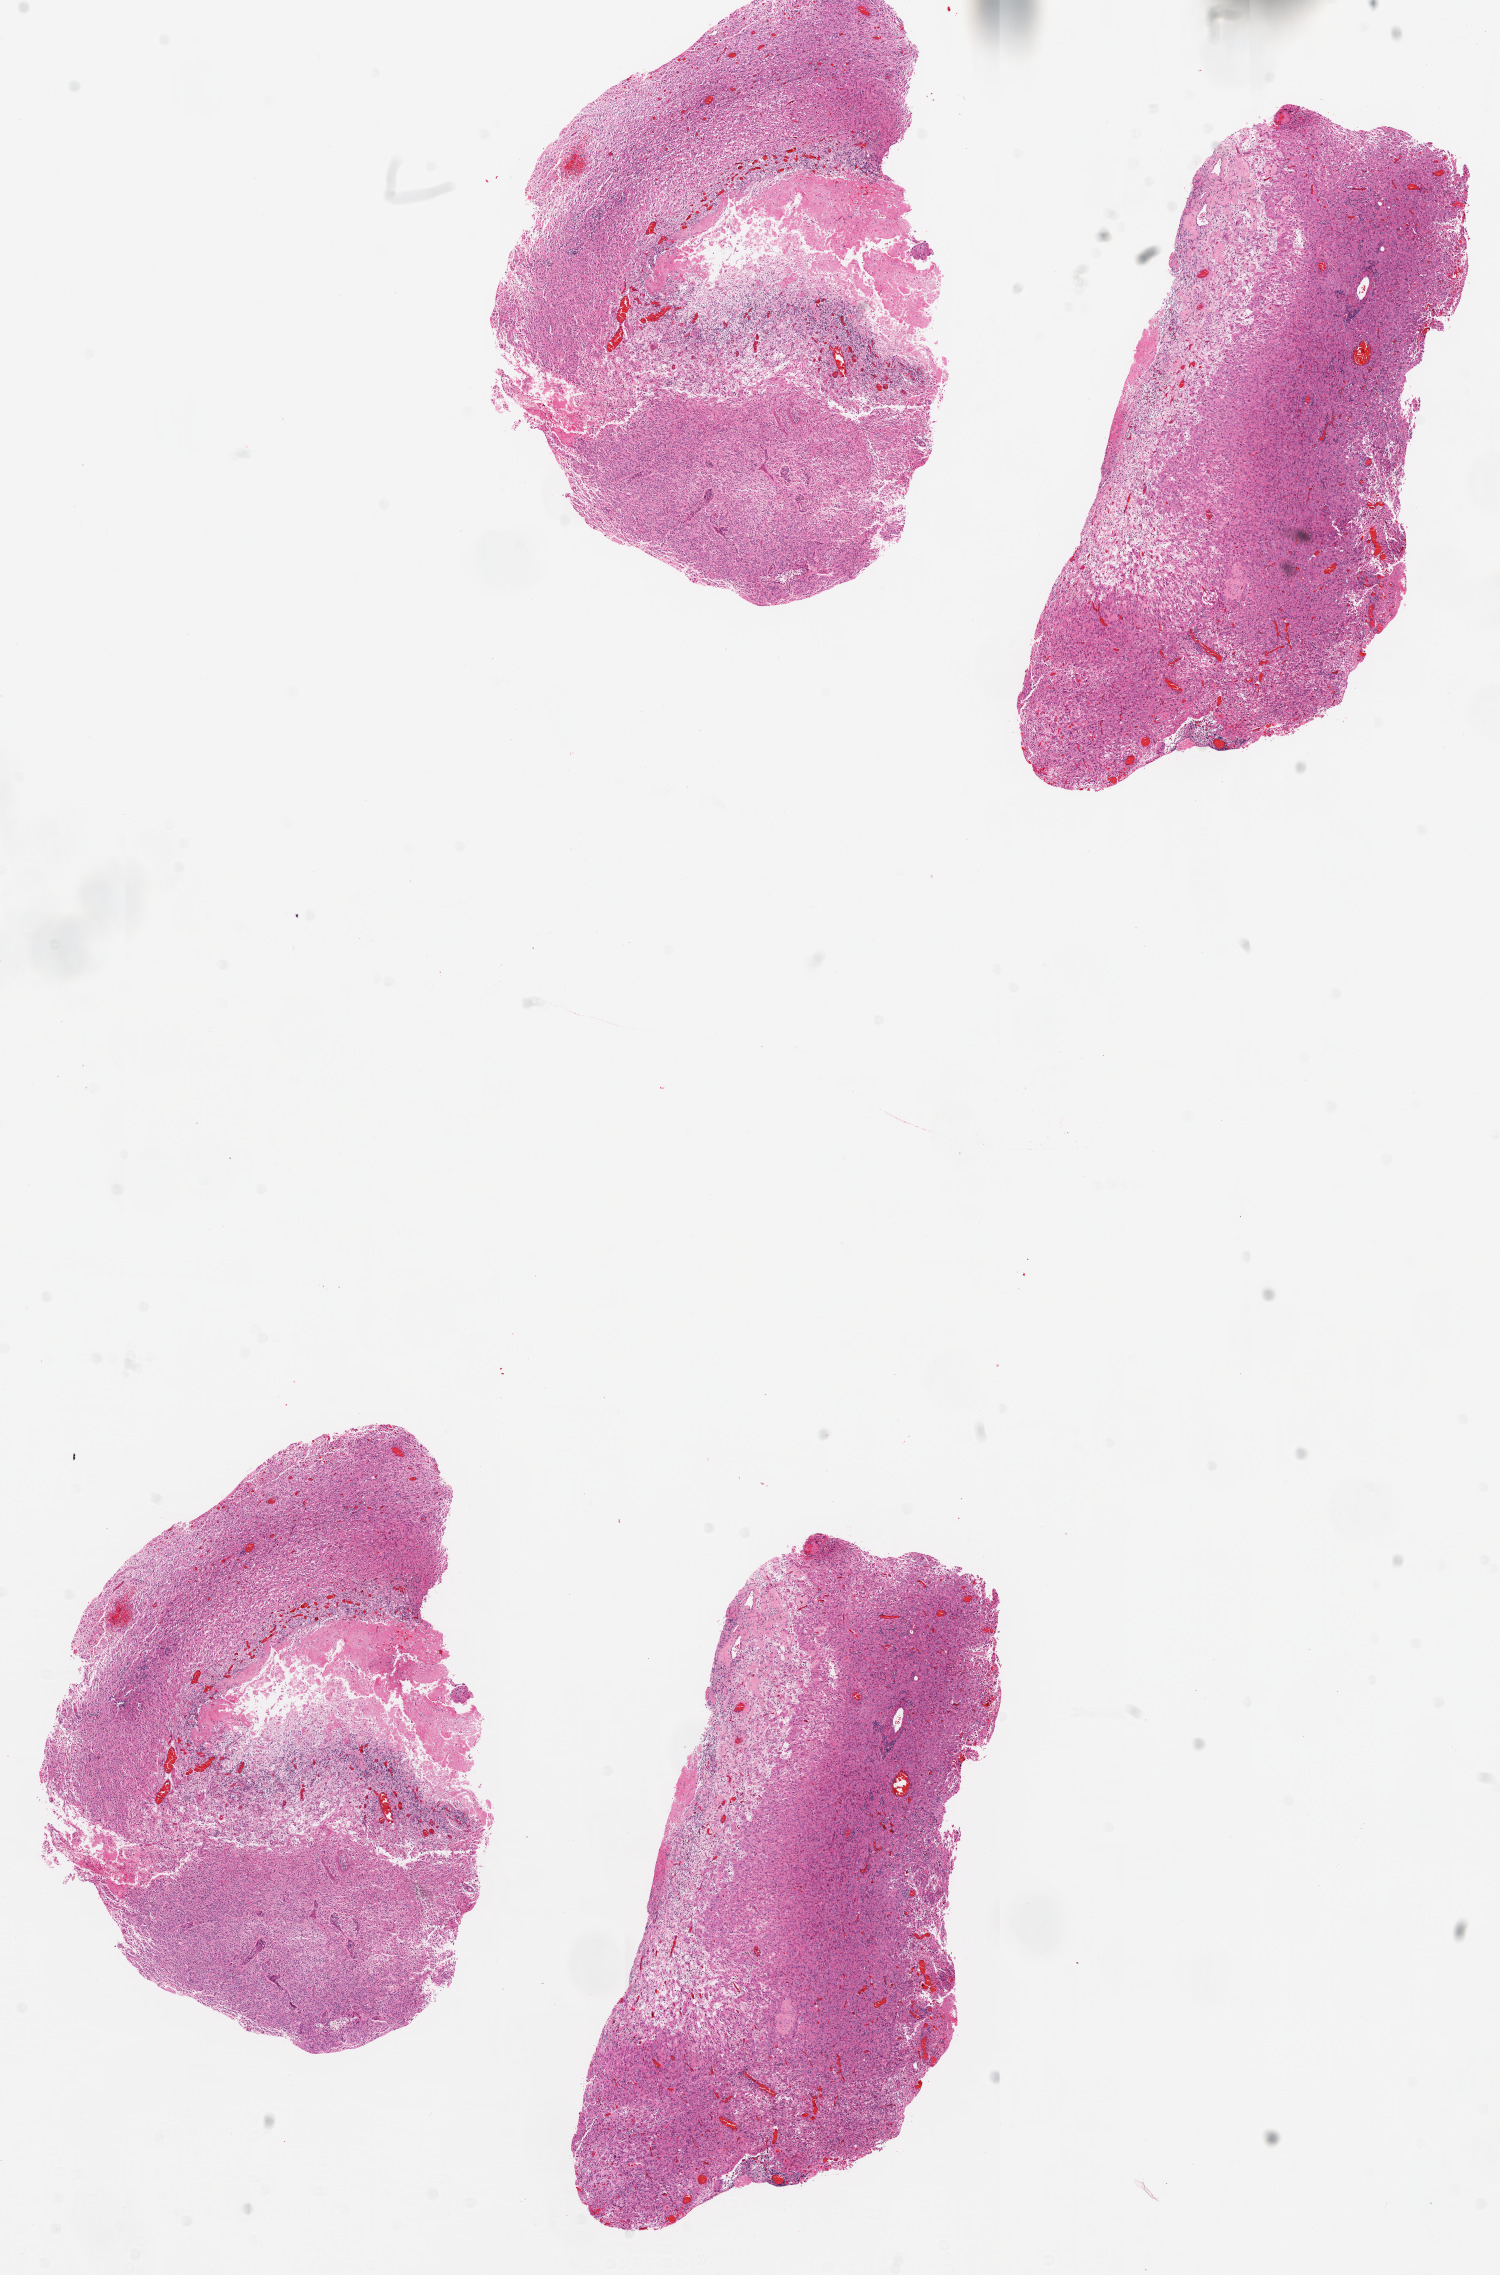
H&E whole-slide image, whole scanned area (about 12.0 x 18.3 mm, acquisition: 20x scan) shown as a low-resolution overview, FFPE section, primary tumour sample from the brain. Patient: male, age at initial diagnosis 76 years.
Diagnosis: Glioblastoma.